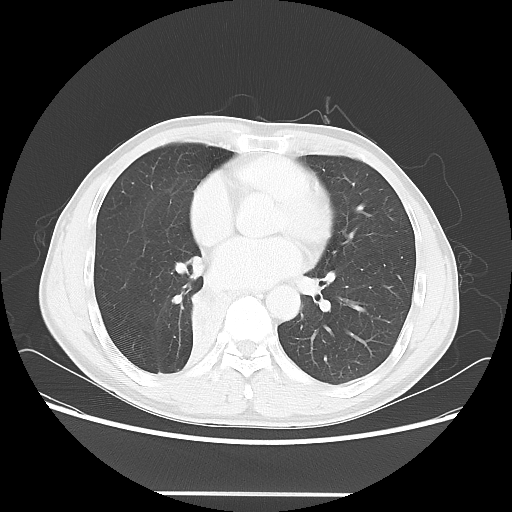
Chest CT, one axial slice; slice 28 of 62 in the series (ordered by position); reconstruction kernel LUNG; lung window (W 1500 / L -600 HU); 5 mm slice thickness; 512 × 512 image matrix, field of view 393 × 393 mm. Male patient, age 47 years. Case-level facts recorded for this patient, not image findings: clinical TNM (as recorded): T2 N0 M0; histopathological grade: G2.
Outlined on this slice (bounding box drawn by a radiologist):
- lung tumour (recorded histology: squamous cell carcinoma): bounding box (x1, y1, x2, y2) in pixels: (188, 280, 237, 344)